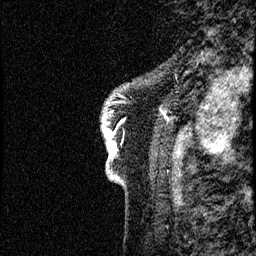
Breast MRI (dynamic contrast-enhanced), one sagittal slice; position 5 of 60 along the scan axis; dynamic contrast-enhanced study with each time point stored as its own series, time point 2 of 4 at this slice position (early post-contrast, ordered by acquisition time); 1.5 T; TE 4.2 ms, TR 17.6 ms; 2 mm slice thickness; 256 × 256 image matrix, field of view 200 × 200 mm. Patient: female, 40 years. Case-level facts recorded for this patient, not image findings: setting: breast cancer imaged before/during neoadjuvant chemotherapy; receptor status: HER2-positive.
Annotated regions visible in this slice (semi-automatic segmentation, software-assisted and operator-edited):
- analysis volume of interest (the breast-tissue region the enhancement analysis was run in; not a lesion): bounding box (x1, y1, x2, y2) in pixels: (97, 58, 185, 204)
- tumour enhancement mask (voxels above the 100 % enhancement threshold inside the analysis volume of interest): (102, 101, 160, 157)